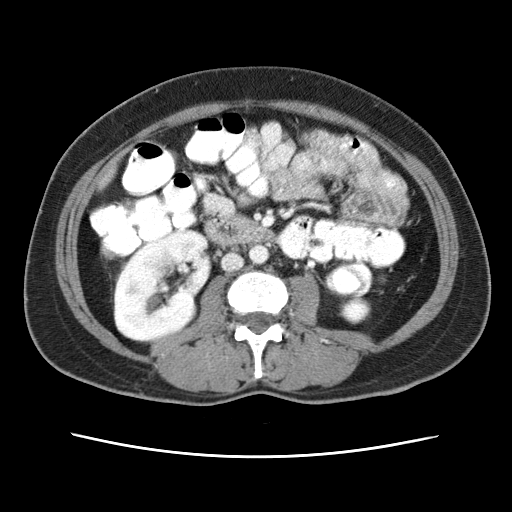
Contrast-enhanced abdominal CT (liver protocol), one axial slice. Position 1 of 79 along the scan axis. Reconstruction kernel STANDARD. Soft-tissue window (W 400 / L 40 HU). 2.5 mm slice thickness. 512 × 512 image matrix. Case-level facts recorded for this patient, not image findings: diagnosis: hepatocellular carcinoma (patient treated with transarterial chemoembolisation; whether this scan precedes or follows treatment is not stated here); TNM stage (as recorded): Stage-I.
Outlined on this slice (semi-automatic segmentation, software-assisted and operator-edited):
- abdominal aorta: box from (x=248, y=245) to (x=268, y=264) px